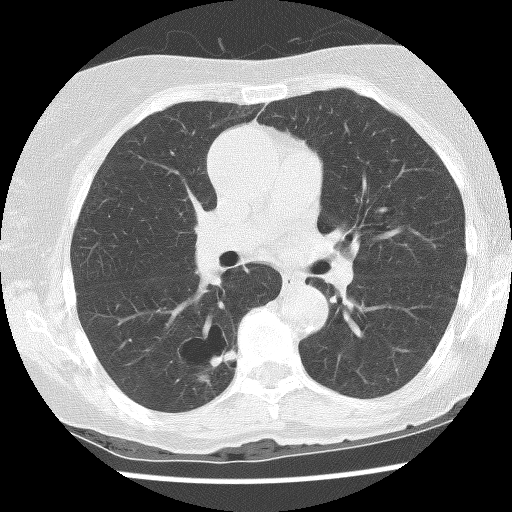
Axial slice from a low-dose chest CT screening exam; baseline screening round; lung window (W 1500 / L -600 HU); lung (sharp) reconstruction kernel (BONE); 512 × 512 image matrix, field of view 300 × 300 mm. Female participant, aged 69 years at enrolment. Former smoker at enrolment.
- Expert-annotated lung lesion, bounding box (x1, y1, x2, y2) in pixels: (154, 319, 248, 395).
- The screening reader recorded 2 non-calcified nodules or masses ≥4 mm on this exam (right lower lobe, right lower lobe); which of them this box marks is not recorded.
- Official screen result: positive, change unspecified: nodule(s) >= 4 mm or enlarging nodule(s), mass(es), or other non-specific abnormalities suspicious for lung cancer.
- Participant outcome: lung cancer diagnosed 288 days after this screen — non-small cell carcinoma, right lower lobe, poorly differentiated (G3), stage IB (AJCC 6th edition), 36 mm at pathology.